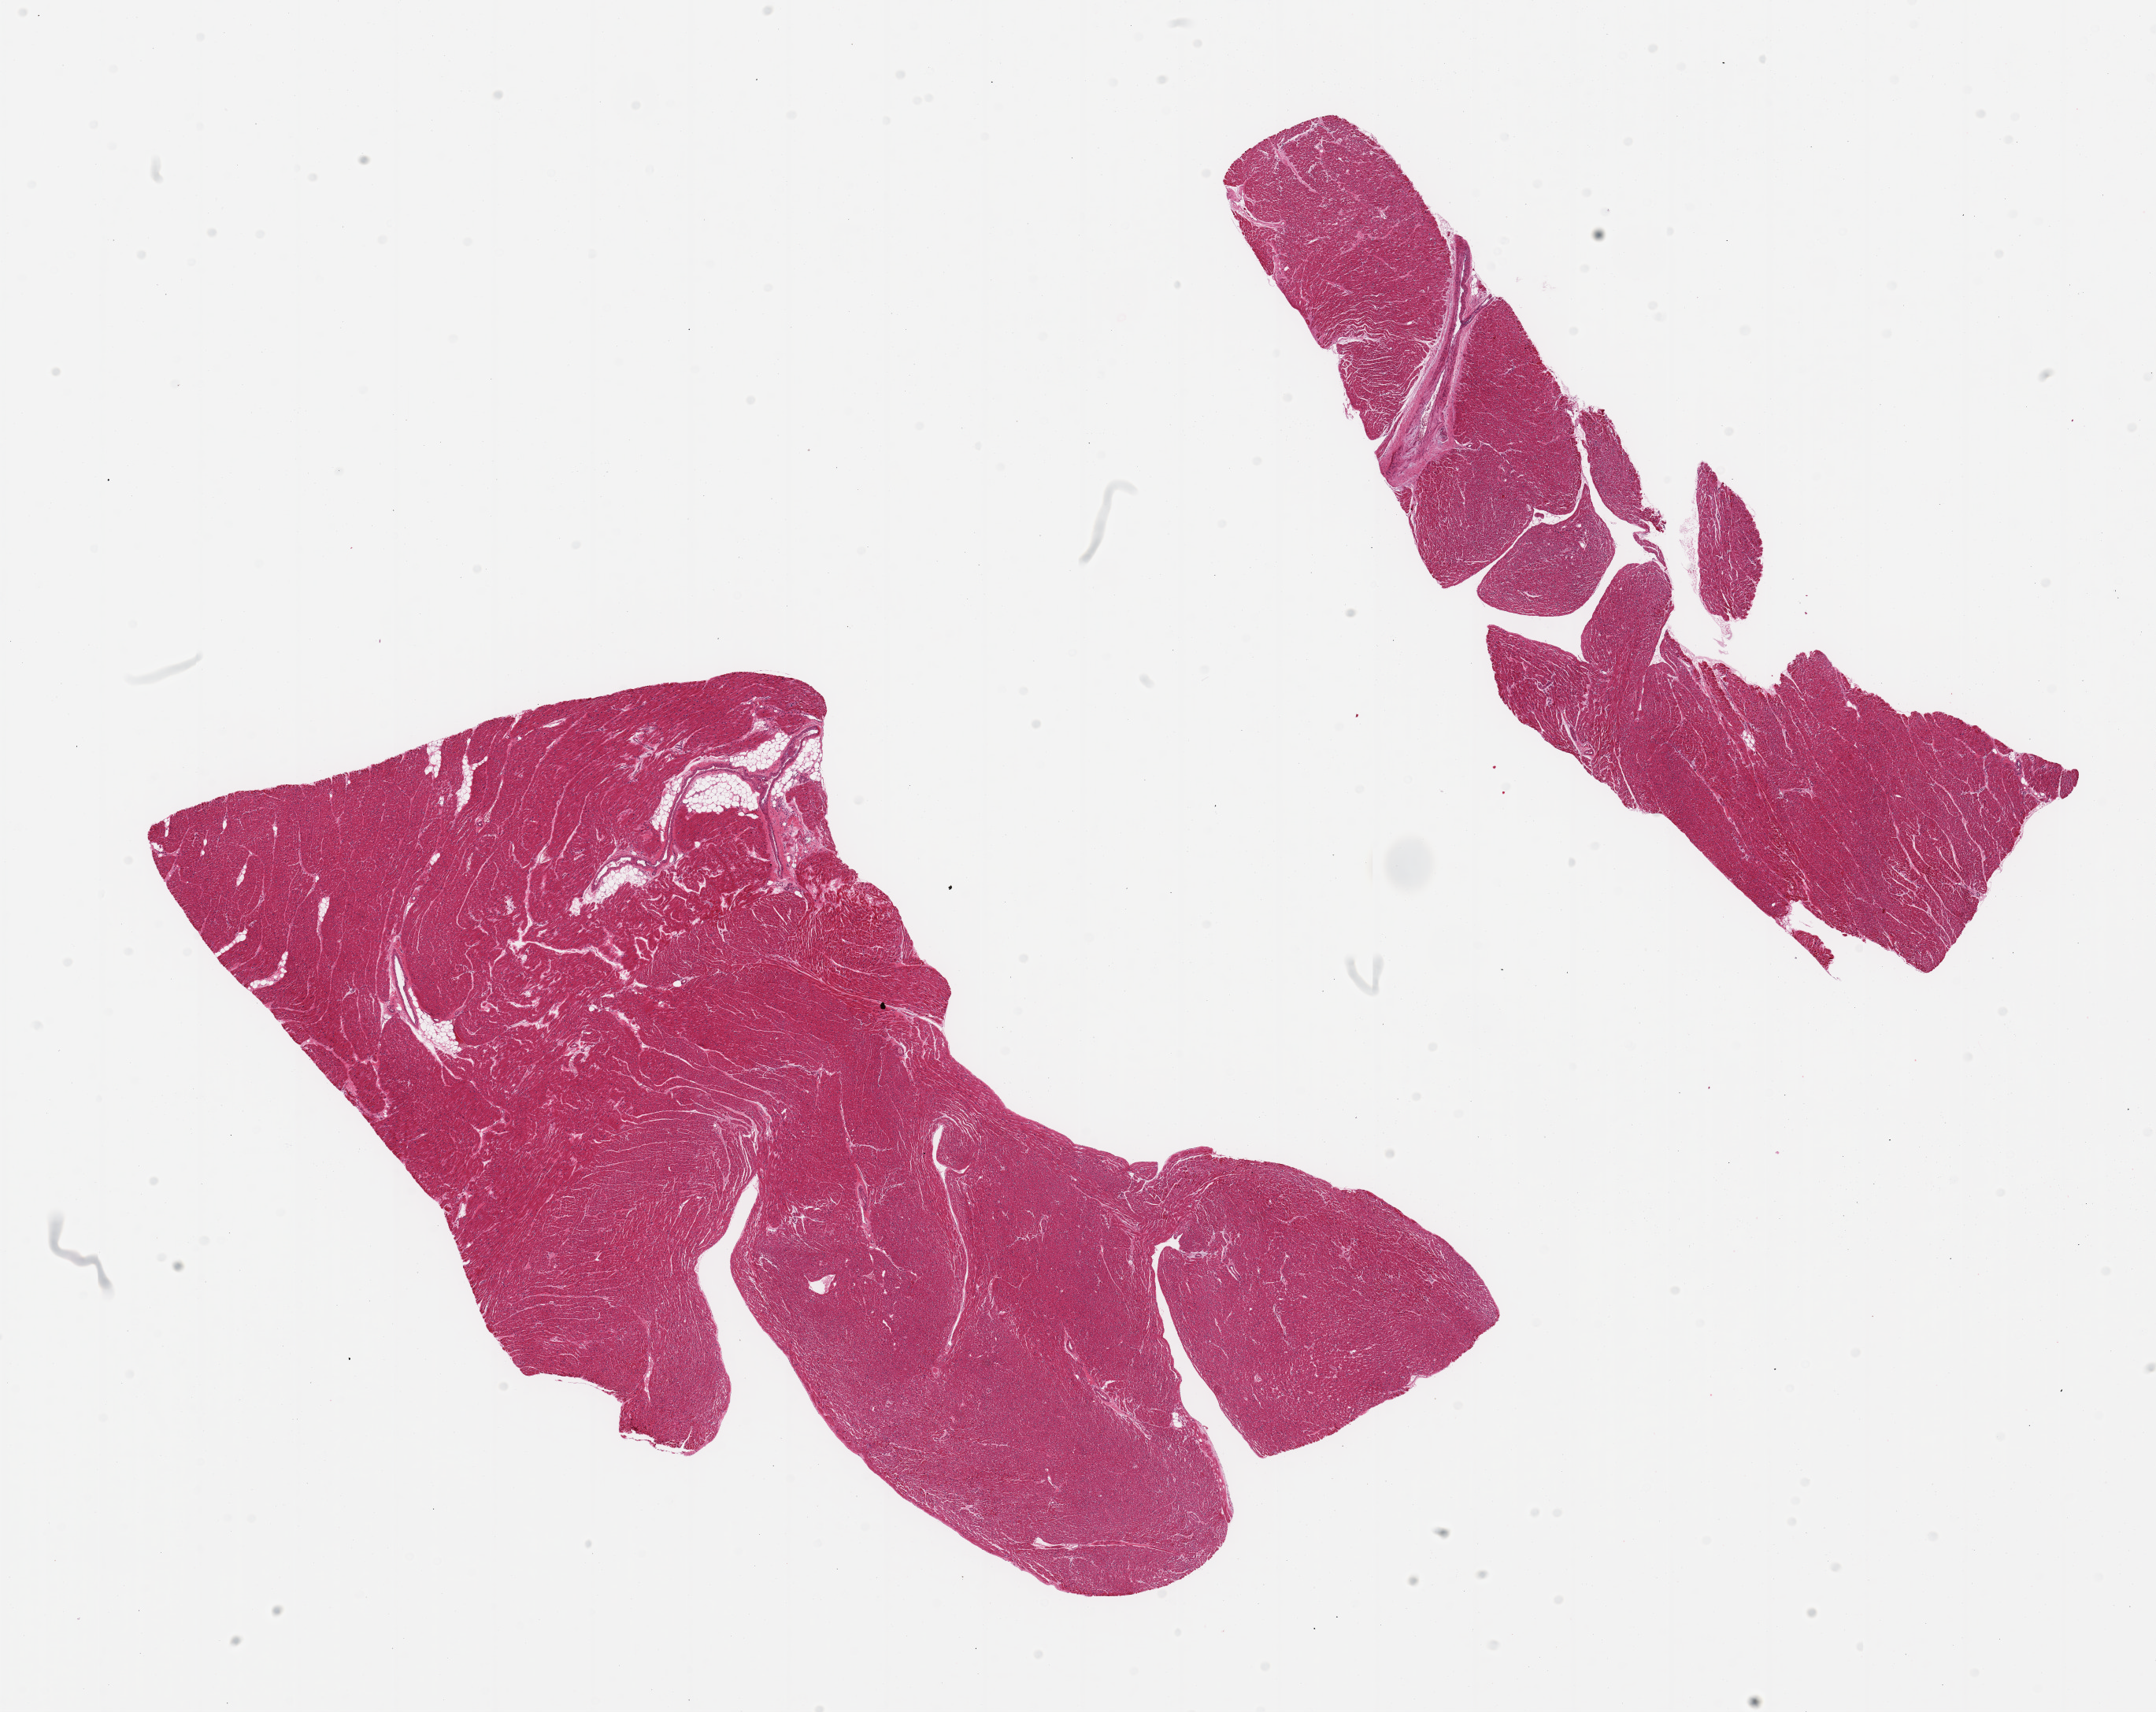
Hematoxylin and eosin (H&E) whole-slide image, low-resolution overview of the scanned area, about 21.7 x 17.2 mm, PAXgene-fixed, paraffin-embedded tissue, sampled site (target tissue): heart, tissue donor sample. Female donor.
Reviewer comment on this tissue sample: 2 pieces; artery bisects smaller piece; no lesions.